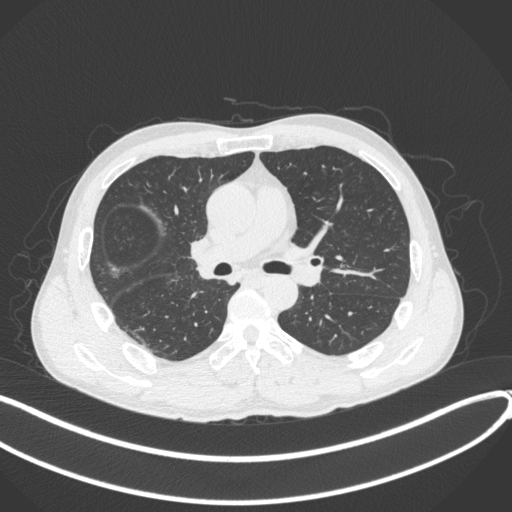
Chest CT, one axial slice. Slice 226 of 409 in the series (ordered by position). Reconstruction kernel B31f. Lung window (W 1500 / L -600 HU). 1 mm slice thickness. 512 × 512 image matrix. Male patient, age 53 years. Case-level facts recorded for this patient, not image findings: clinical TNM (as recorded): T1b N0 M0.
Annotated regions visible in this slice (bounding box drawn by a radiologist):
- lung tumour (recorded histology: squamous cell carcinoma): bounding box <187,229,227,284> (left, top, right, bottom; pixels)